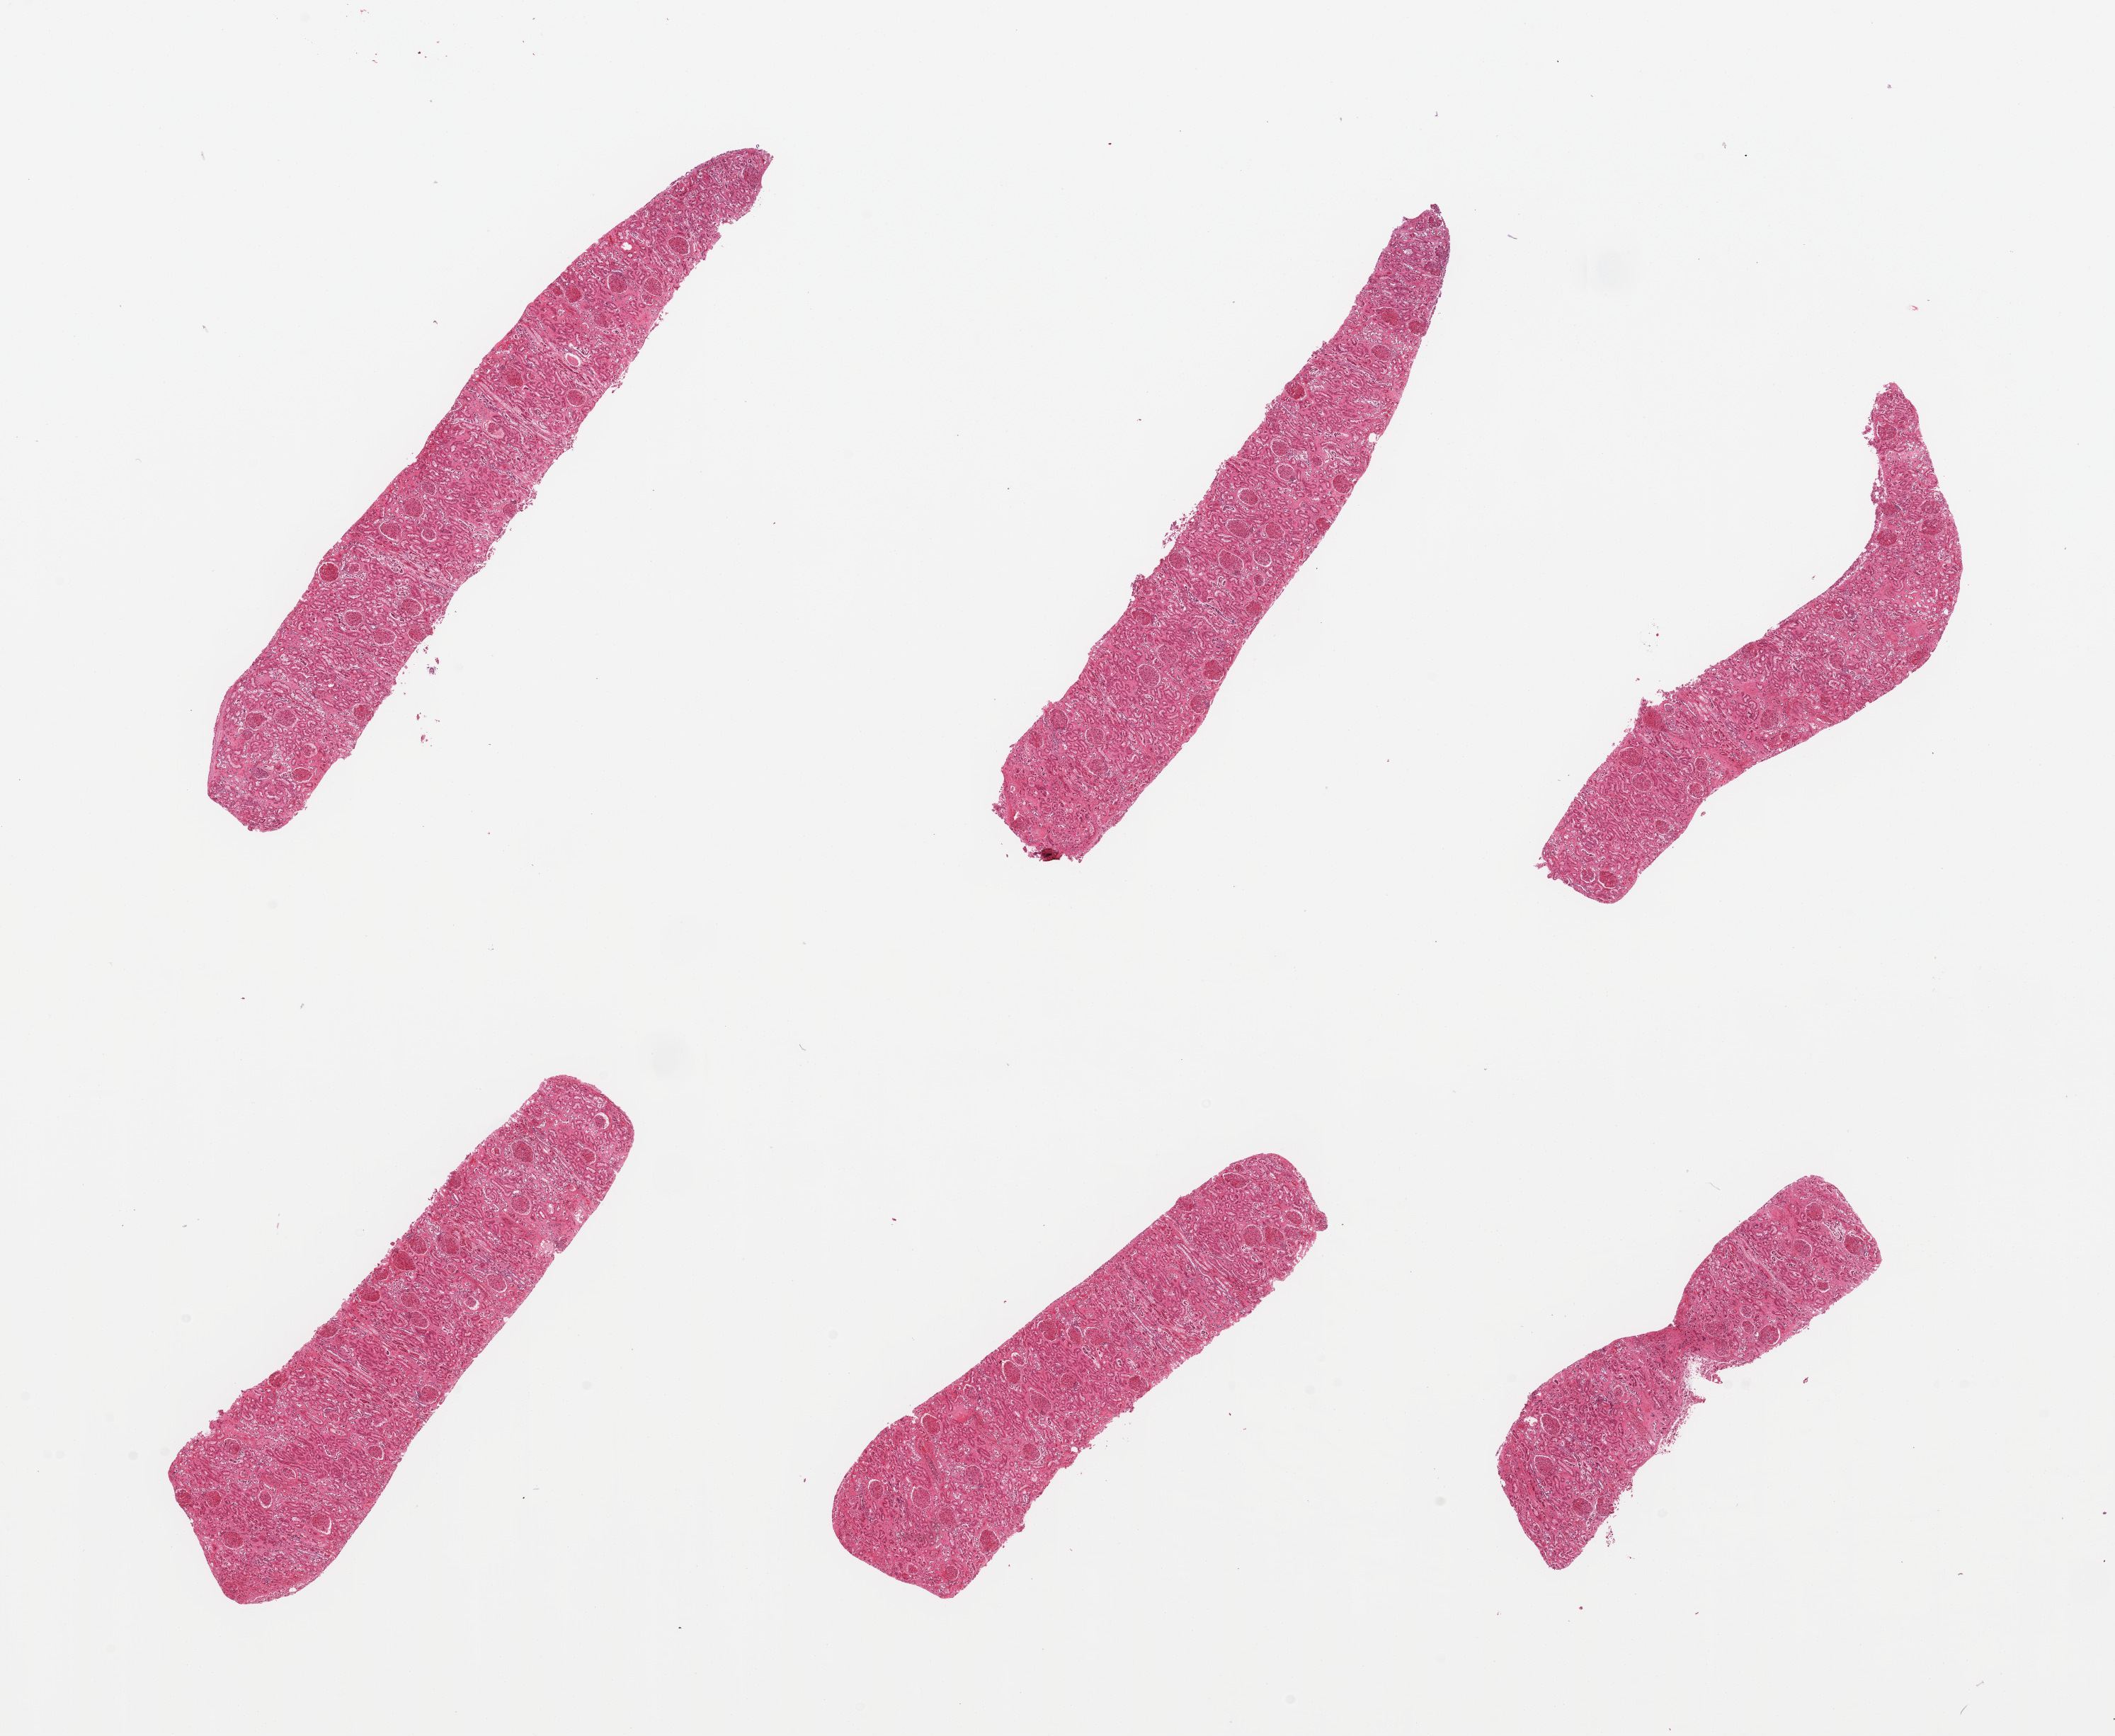
H&E whole-slide image, brightfield — low-resolution overview of the scanned area, about 23.6 x 19.4 mm (slide scanned at 20x). PAXgene-fixed, paraffin-embedded tissue. Section of renal cortex (target tissue). Donor tissue sample. Donor: male.
Review note (as recorded): 6 pieces, glomeruli present; tubules with advance autolysis/sloughing.